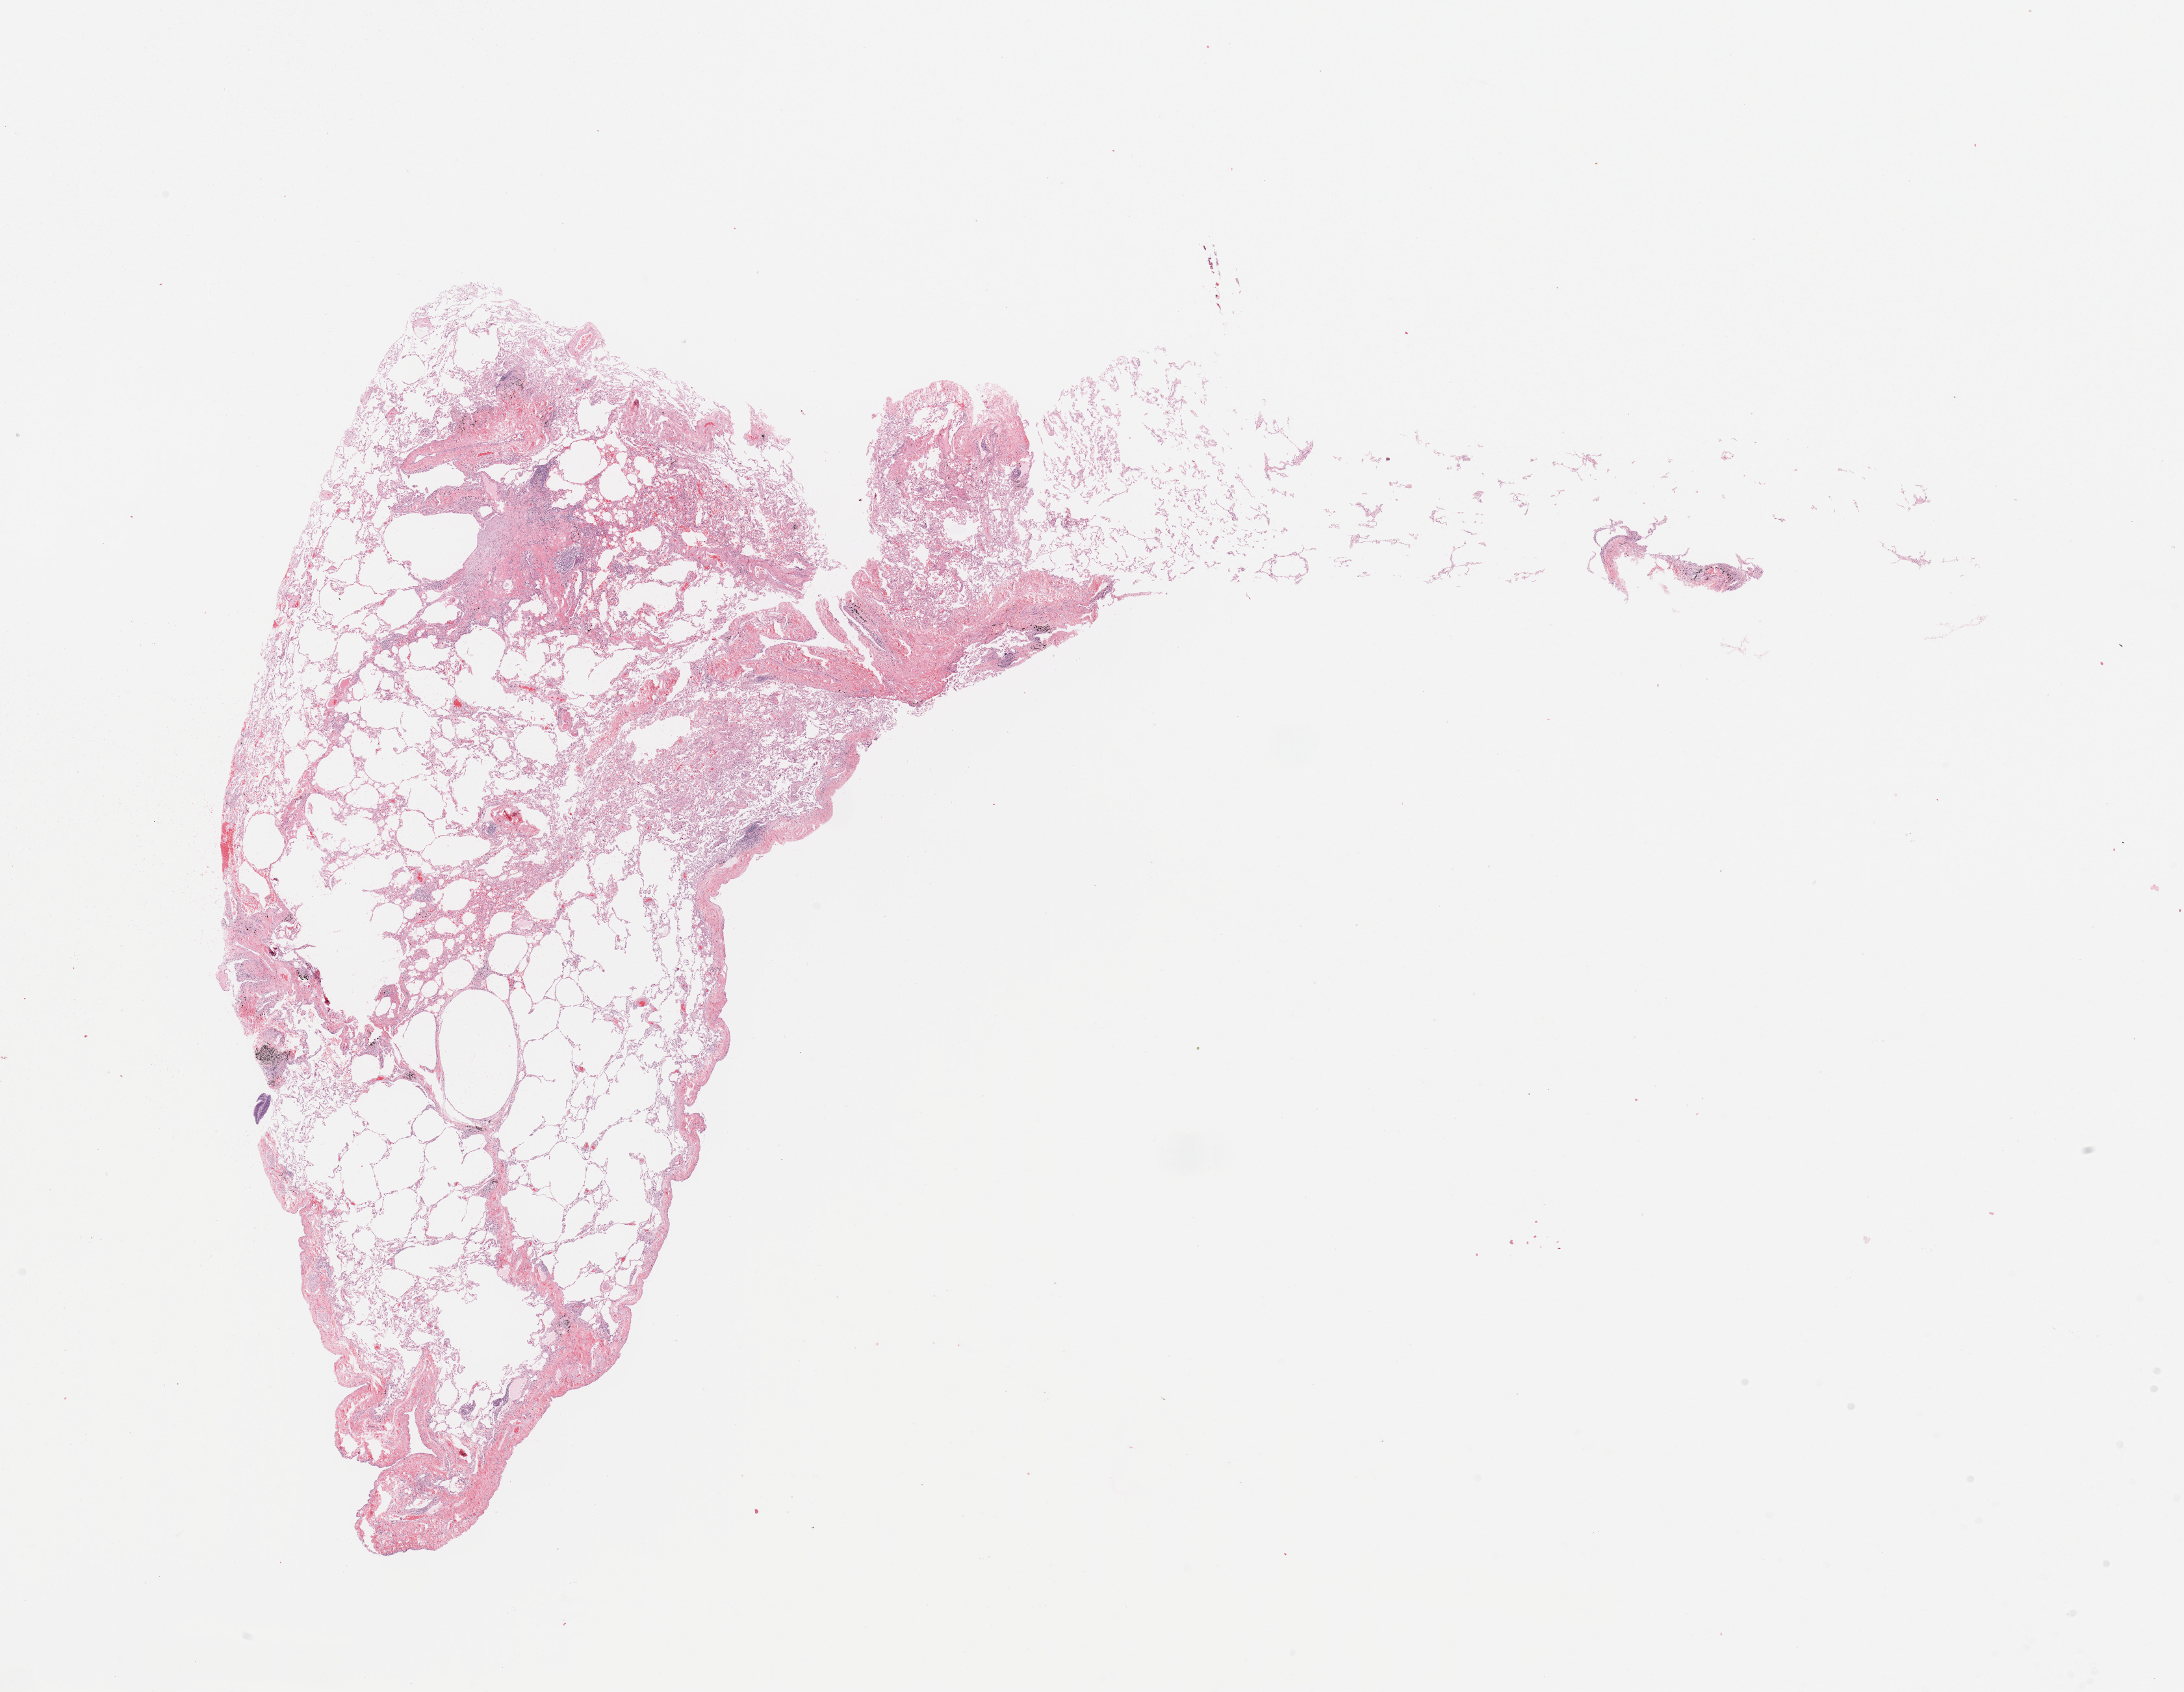
H&E whole-slide image — low-resolution overview of the scanned area, about 26.6 x 20.6 mm (acquisition: 20x scan), normal (non-tumour) tissue sample, sampled site: lung. Male, 64 y/o.
This section: normal (non-tumour) tissue from the same patient. Patient diagnosis: Adenocarcinoma, NOS.